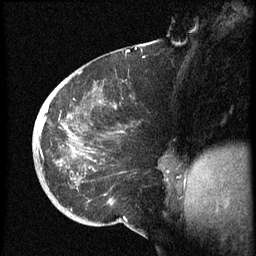
Breast MRI (dynamic contrast-enhanced), one sagittal slice; slice 25 of 60 in the series (ordered by position); dynamic contrast-enhanced series, image 2 of 3 at this slice position (ordered by acquisition); 1.5 T; TE 4.2 ms, TR 8.4 ms; 2.5 mm slice thickness; 256 × 256 image matrix. Patient: female, 38 years. Case-level facts recorded for this patient, not image findings: setting: breast cancer imaged before/during neoadjuvant chemotherapy; receptor status: HER2-positive.
Outlined on this slice (semi-automatically segmented with operator editing):
- analysis volume of interest (the breast-tissue region the enhancement analysis was run in; not a lesion): bounding box <33,74,173,202> (left, top, right, bottom; pixels)
- tumour enhancement mask (voxels above the 70 % enhancement threshold inside the analysis volume of interest): <36,105,97,181>